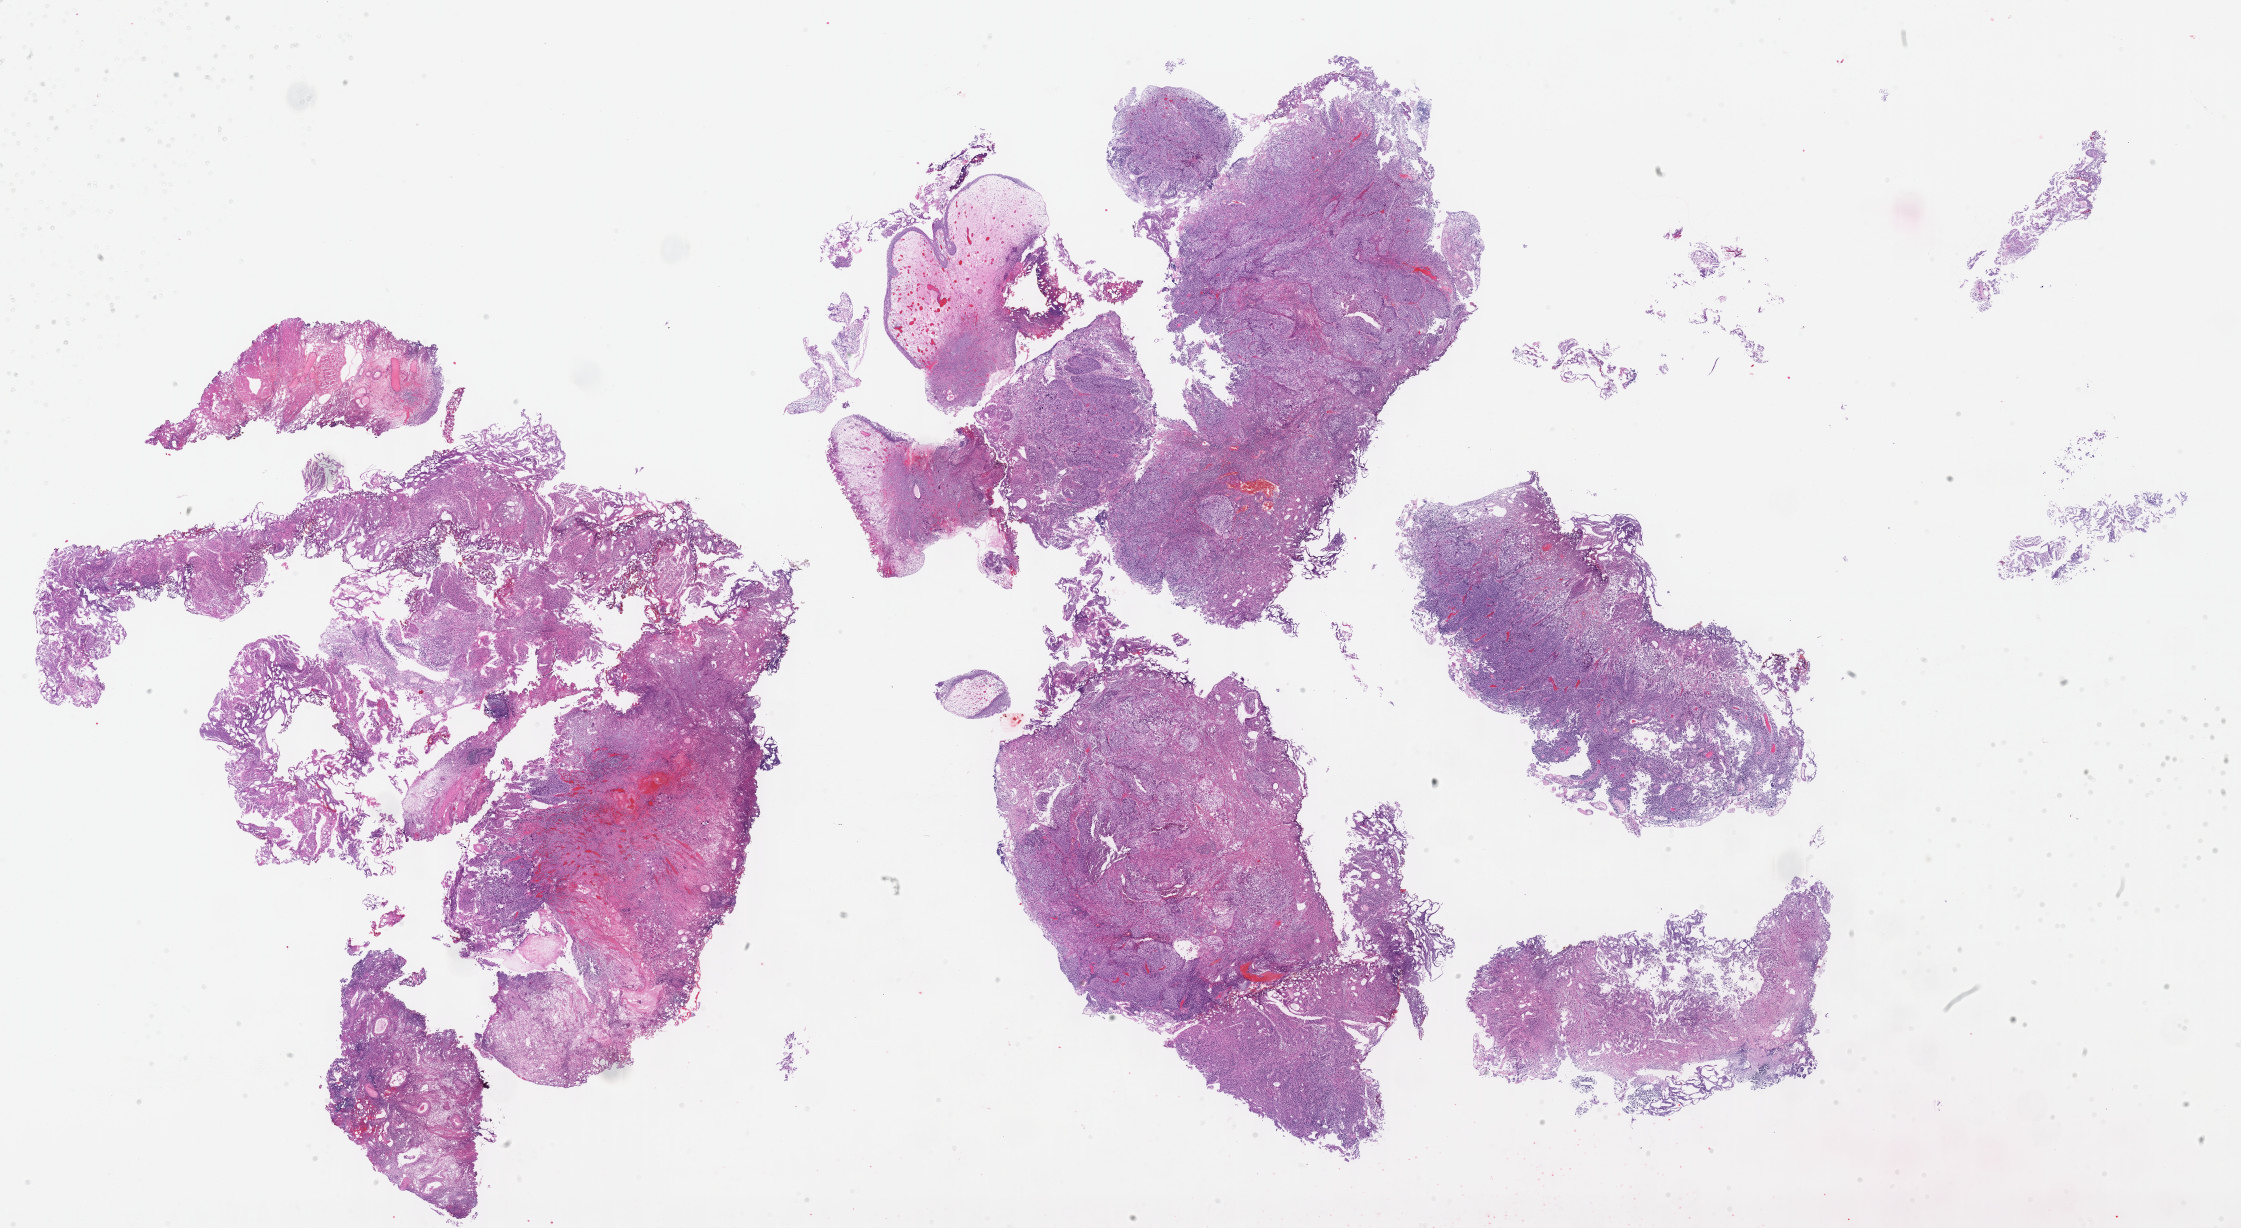
Whole-slide histology image, Hematoxylin and eosin (H&E) stained — whole scanned area (about 36.2 x 19.8 mm, slide scanned at 40x) shown as a low-resolution overview; formalin-fixed paraffin-embedded (FFPE) diagnostic section; bladder, primary tumour sample. Female, age 75 years at initial diagnosis. Histologic grade: high grade.
TNM: T2 N0 M0. Lymph nodes positive (case pathology): 0 of 25 examined. Pathologic diagnosis: Transitional cell carcinoma. AJCC pathologic stage: II (6th edition).